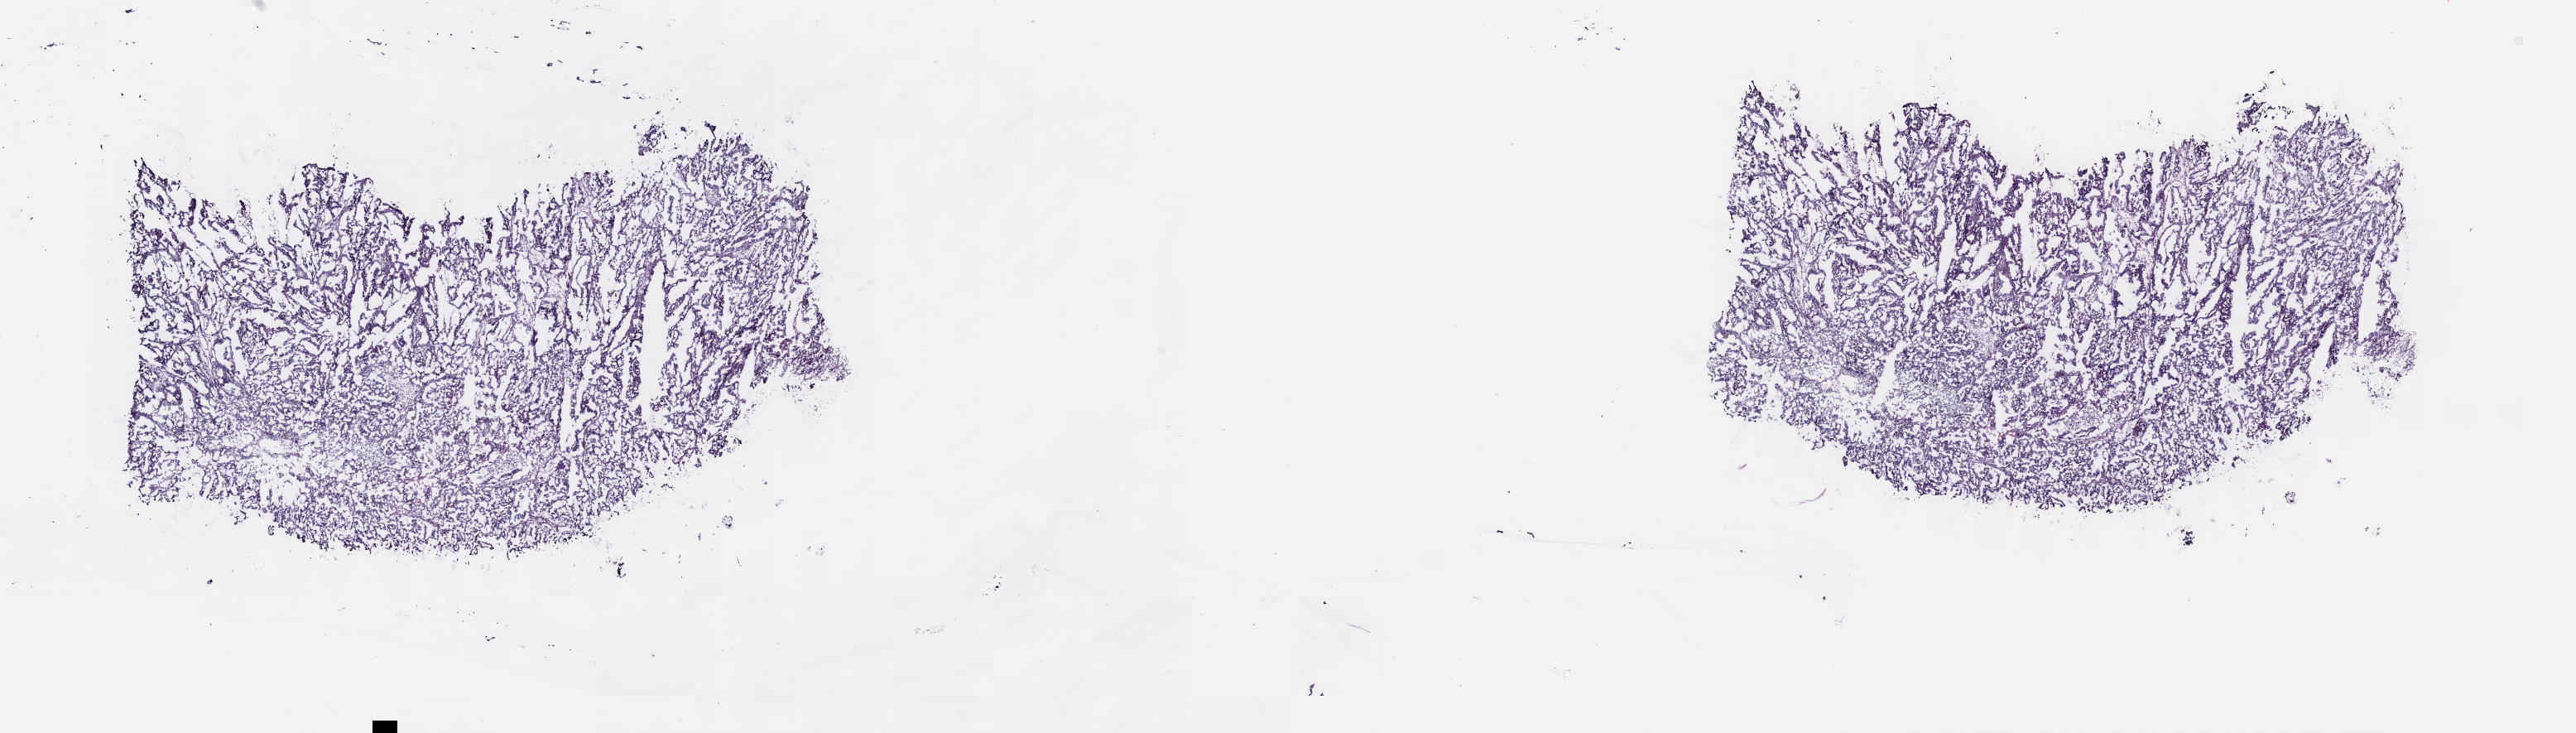
Digitized H&E tissue section (whole slide), low-resolution overview of the scanned area, about 25.2 x 7.2 mm. Frozen section from the top of the tissue portion. Testis, primary tumour sample. Male patient; age at initial diagnosis 18 years. Pathologist review of this section (percent, as recorded): tumour cells 100%, tumour nuclei 75%, normal cells 0%, stromal cells 0%, necrosis 0%. Inflammatory infiltration, as recorded: lymphocyte infiltration 0%, monocyte infiltration 0%, neutrophil infiltration 0%.
AJCC pathologic stage: IA. Histologic diagnosis: Embryonal carcinoma, NOS. Laterality: right.